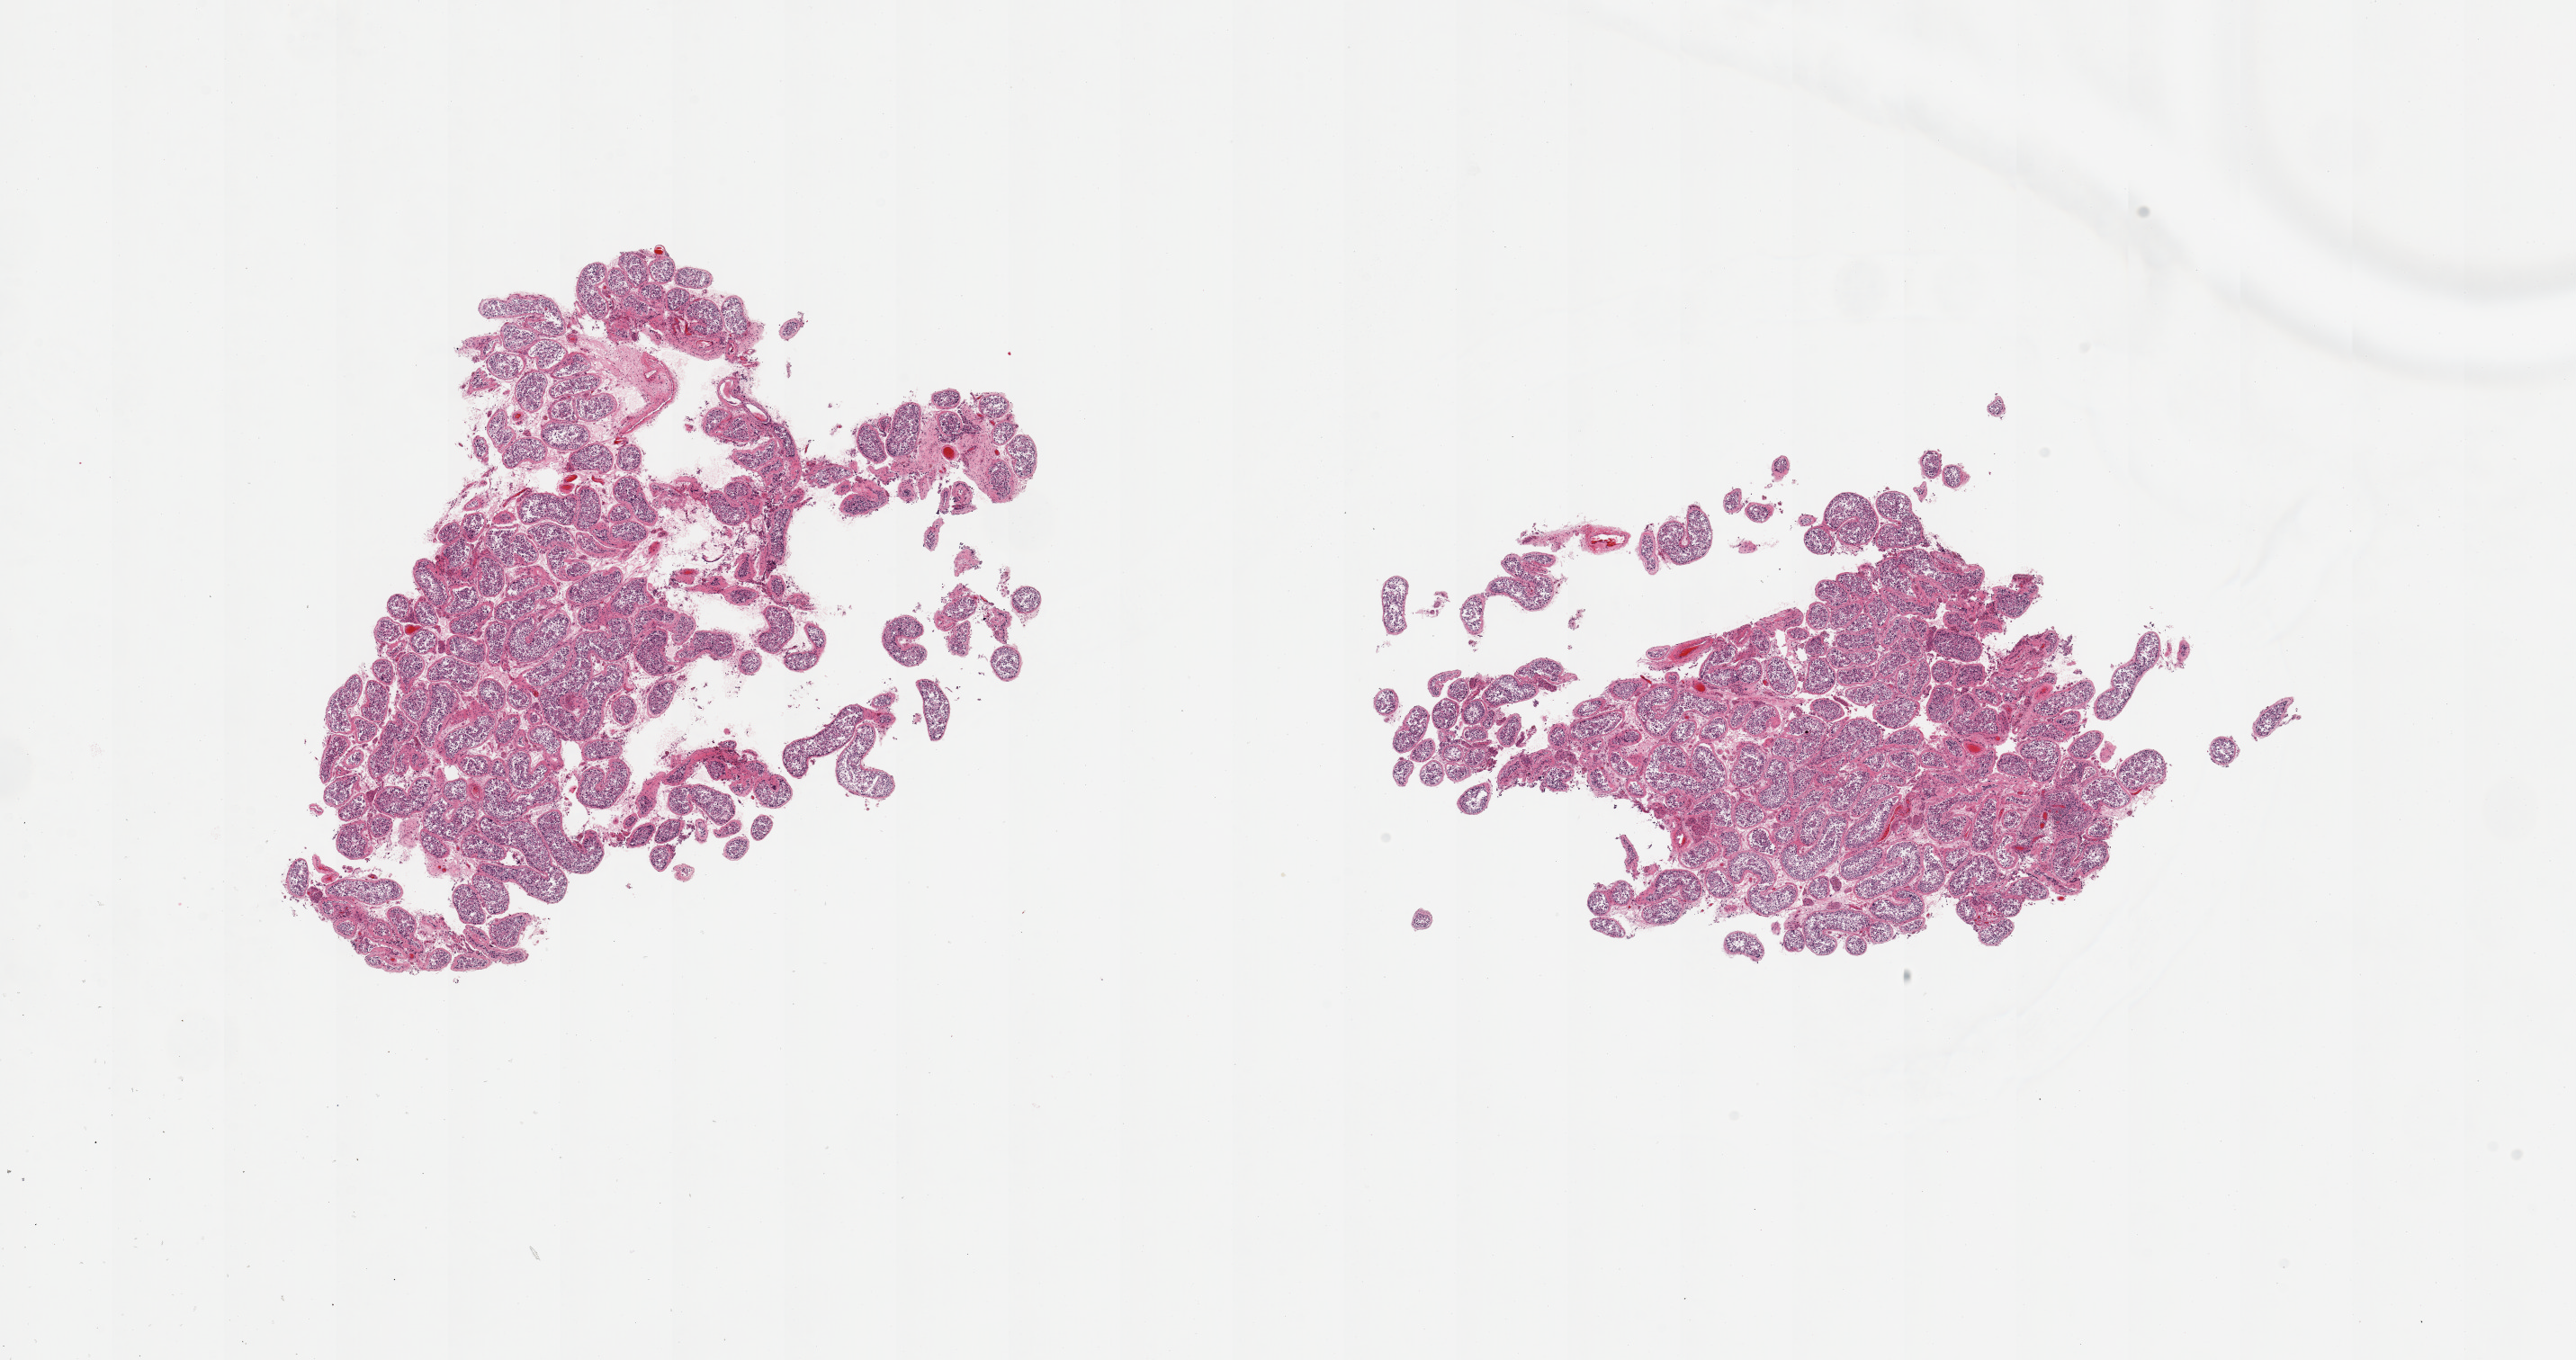
Whole-slide image, haematoxylin and eosin stain, brightfield — whole scanned area (about 22.6 x 12.0 mm, from a 20x scan) shown as a low-resolution overview, PAXgene-fixed paraffin-embedded (PFPE) section, sampled site (target tissue): testis, donor tissue sample. Male donor.
Reviewer comment on this tissue sample: 2 fragmented pieces; spermatogenesis.